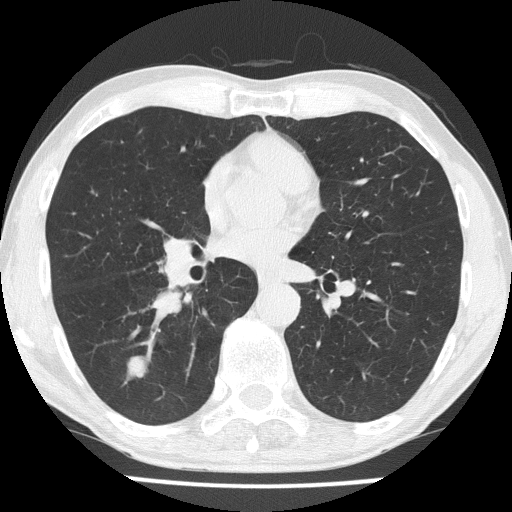
Low-dose screening chest CT, one axial slice. Slice 84 of 186 in the series (ordered by position). Reconstruction kernel FC51. Lung window (W 1500 / L -600 HU). 2 mm slice thickness. 512 × 512 image matrix, field of view 328 × 328 mm.
Annotated regions visible in this slice (manually delineated by an expert):
- lesion 1 (tumor, lower lobe of right lung): bounding box <124,355,148,383> (left, top, right, bottom; pixels)